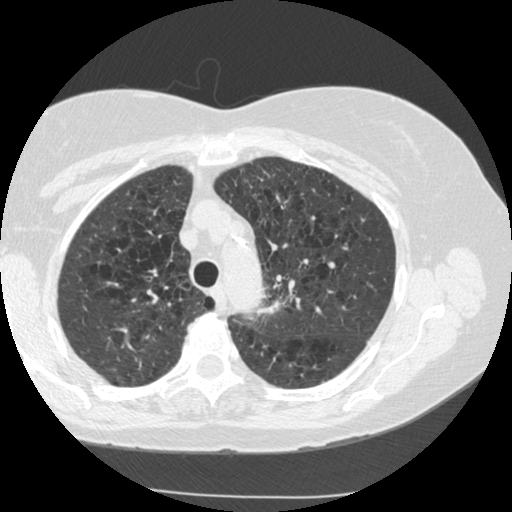
Low-dose screening chest CT, axial slice. Second annual screen. Lung window (W 1500 / L -600 HU). 1.25 mm slice thickness. Standard (soft-tissue) reconstruction kernel (STANDARD). Slice 196 of 249 in the series. 512 × 512 image matrix. Female participant, aged 70 years at enrolment. Current smoker at enrolment.
- Expert-annotated lung lesion, bounding box [x1, y1, x2, y2] px = [236, 271, 297, 336].
- Screening reader's record for this exam (one nodule recorded; not confirmed to be the boxed lesion): non-calcified nodule or mass ≥4 mm, left upper lobe, 15 × 13 mm, spiculated (stellate) margins, soft tissue attenuation, pre-existing on the prior screen: yes; interval growth: yes.
- Official screen result: positive, other.
- Lung cancer was diagnosed 360 days after this screen (after the third annual screen): neoplasm, malignant, left upper lobe, stage IIIB (AJCC 6th edition), 40 mm at pathology.